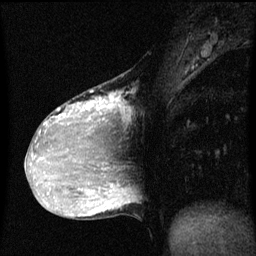
Breast MRI (dynamic contrast-enhanced), one sagittal slice. Position 25 of 60 along the scan axis. Dynamic contrast-enhanced series, image 2 of 3 at this slice position (ordered by acquisition). 1.5 T. TE 4.2 ms, TR 8 ms. 2 mm slice thickness. 256 × 256 image matrix, field of view 200 × 200 mm. Female patient, age 36 years.
Outlined on this slice (semi-automatically segmented with operator editing):
- analysis volume of interest (the breast-tissue region the enhancement analysis was run in; not a lesion): box from (x=33, y=72) to (x=128, y=169) px
- tumour enhancement mask (voxels above the 70 % enhancement threshold inside the analysis volume of interest): (x=36, y=98)–(x=119, y=169)